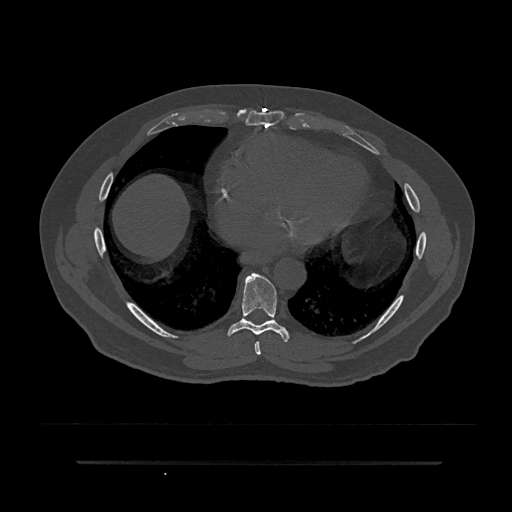
CT including the spine, one axial slice. Slice 430 of 797 in the series (ordered by position). Bone window (W 1800 / L 400 HU). 0.5 mm slice thickness. 512 × 512 image matrix. Patient: male, 59 years. Case-level facts recorded for this patient, not image findings: primary cancer: bile ducts; vertebrae with lytic lesions (as recorded): T10.
Outlined on this slice (semi-automatically segmented with operator editing):
- T7 vertebra: bounding box <254,341,261,355> (left, top, right, bottom; pixels)
- T8 vertebra: <228,273,290,342>